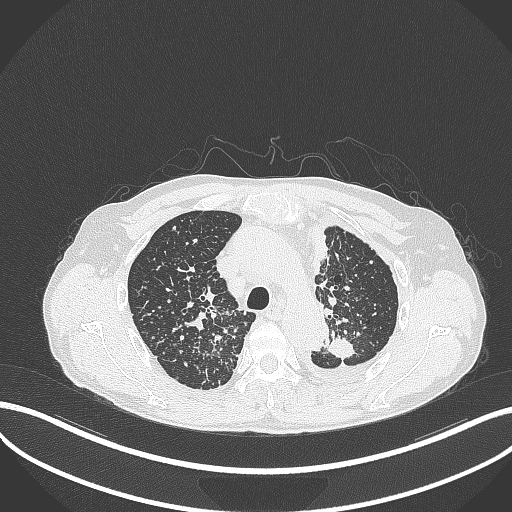
Chest CT, one axial slice; slice 261 of 325 in the series (ordered by position); reconstruction kernel B70f; 120 kVp; lung window (W 1500 / L -600 HU); 1 mm slice thickness; 512 × 512 image matrix, field of view 400 × 400 mm. Patient: male, 58 years. Case-level facts recorded for this patient, not image findings: clinical TNM (as recorded): T1c N3 M1.
Annotated regions visible in this slice (rectangle marked by the reading radiologist):
- lung tumour (recorded histology: adenocarcinoma): bounding box [x1, y1, x2, y2] px = [323, 335, 359, 361]